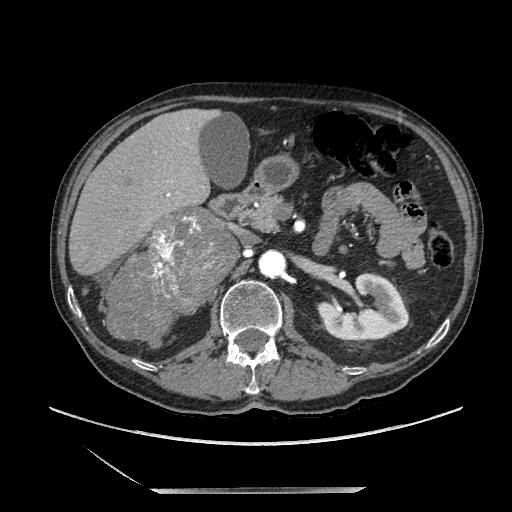
Contrast-enhanced abdominal CT, one axial slice; slice 107 of 243 in the series (ordered by position); soft-tissue window (W 400 / L 40 HU); 1.25 mm slice thickness; 512 × 512 image matrix, field of view 420 × 420 mm. Male patient. Case-level facts recorded for this patient, not image findings: diagnosis: adrenocortical carcinoma; tumour side: right adrenal; tumour size at pathology: 16 cm; Ki-67 index: 17 %; stage (as recorded): 3.
Structures marked on this image (semi-automatically segmented with operator editing):
- mass: bounding box <110,211,231,336> (left, top, right, bottom; pixels)